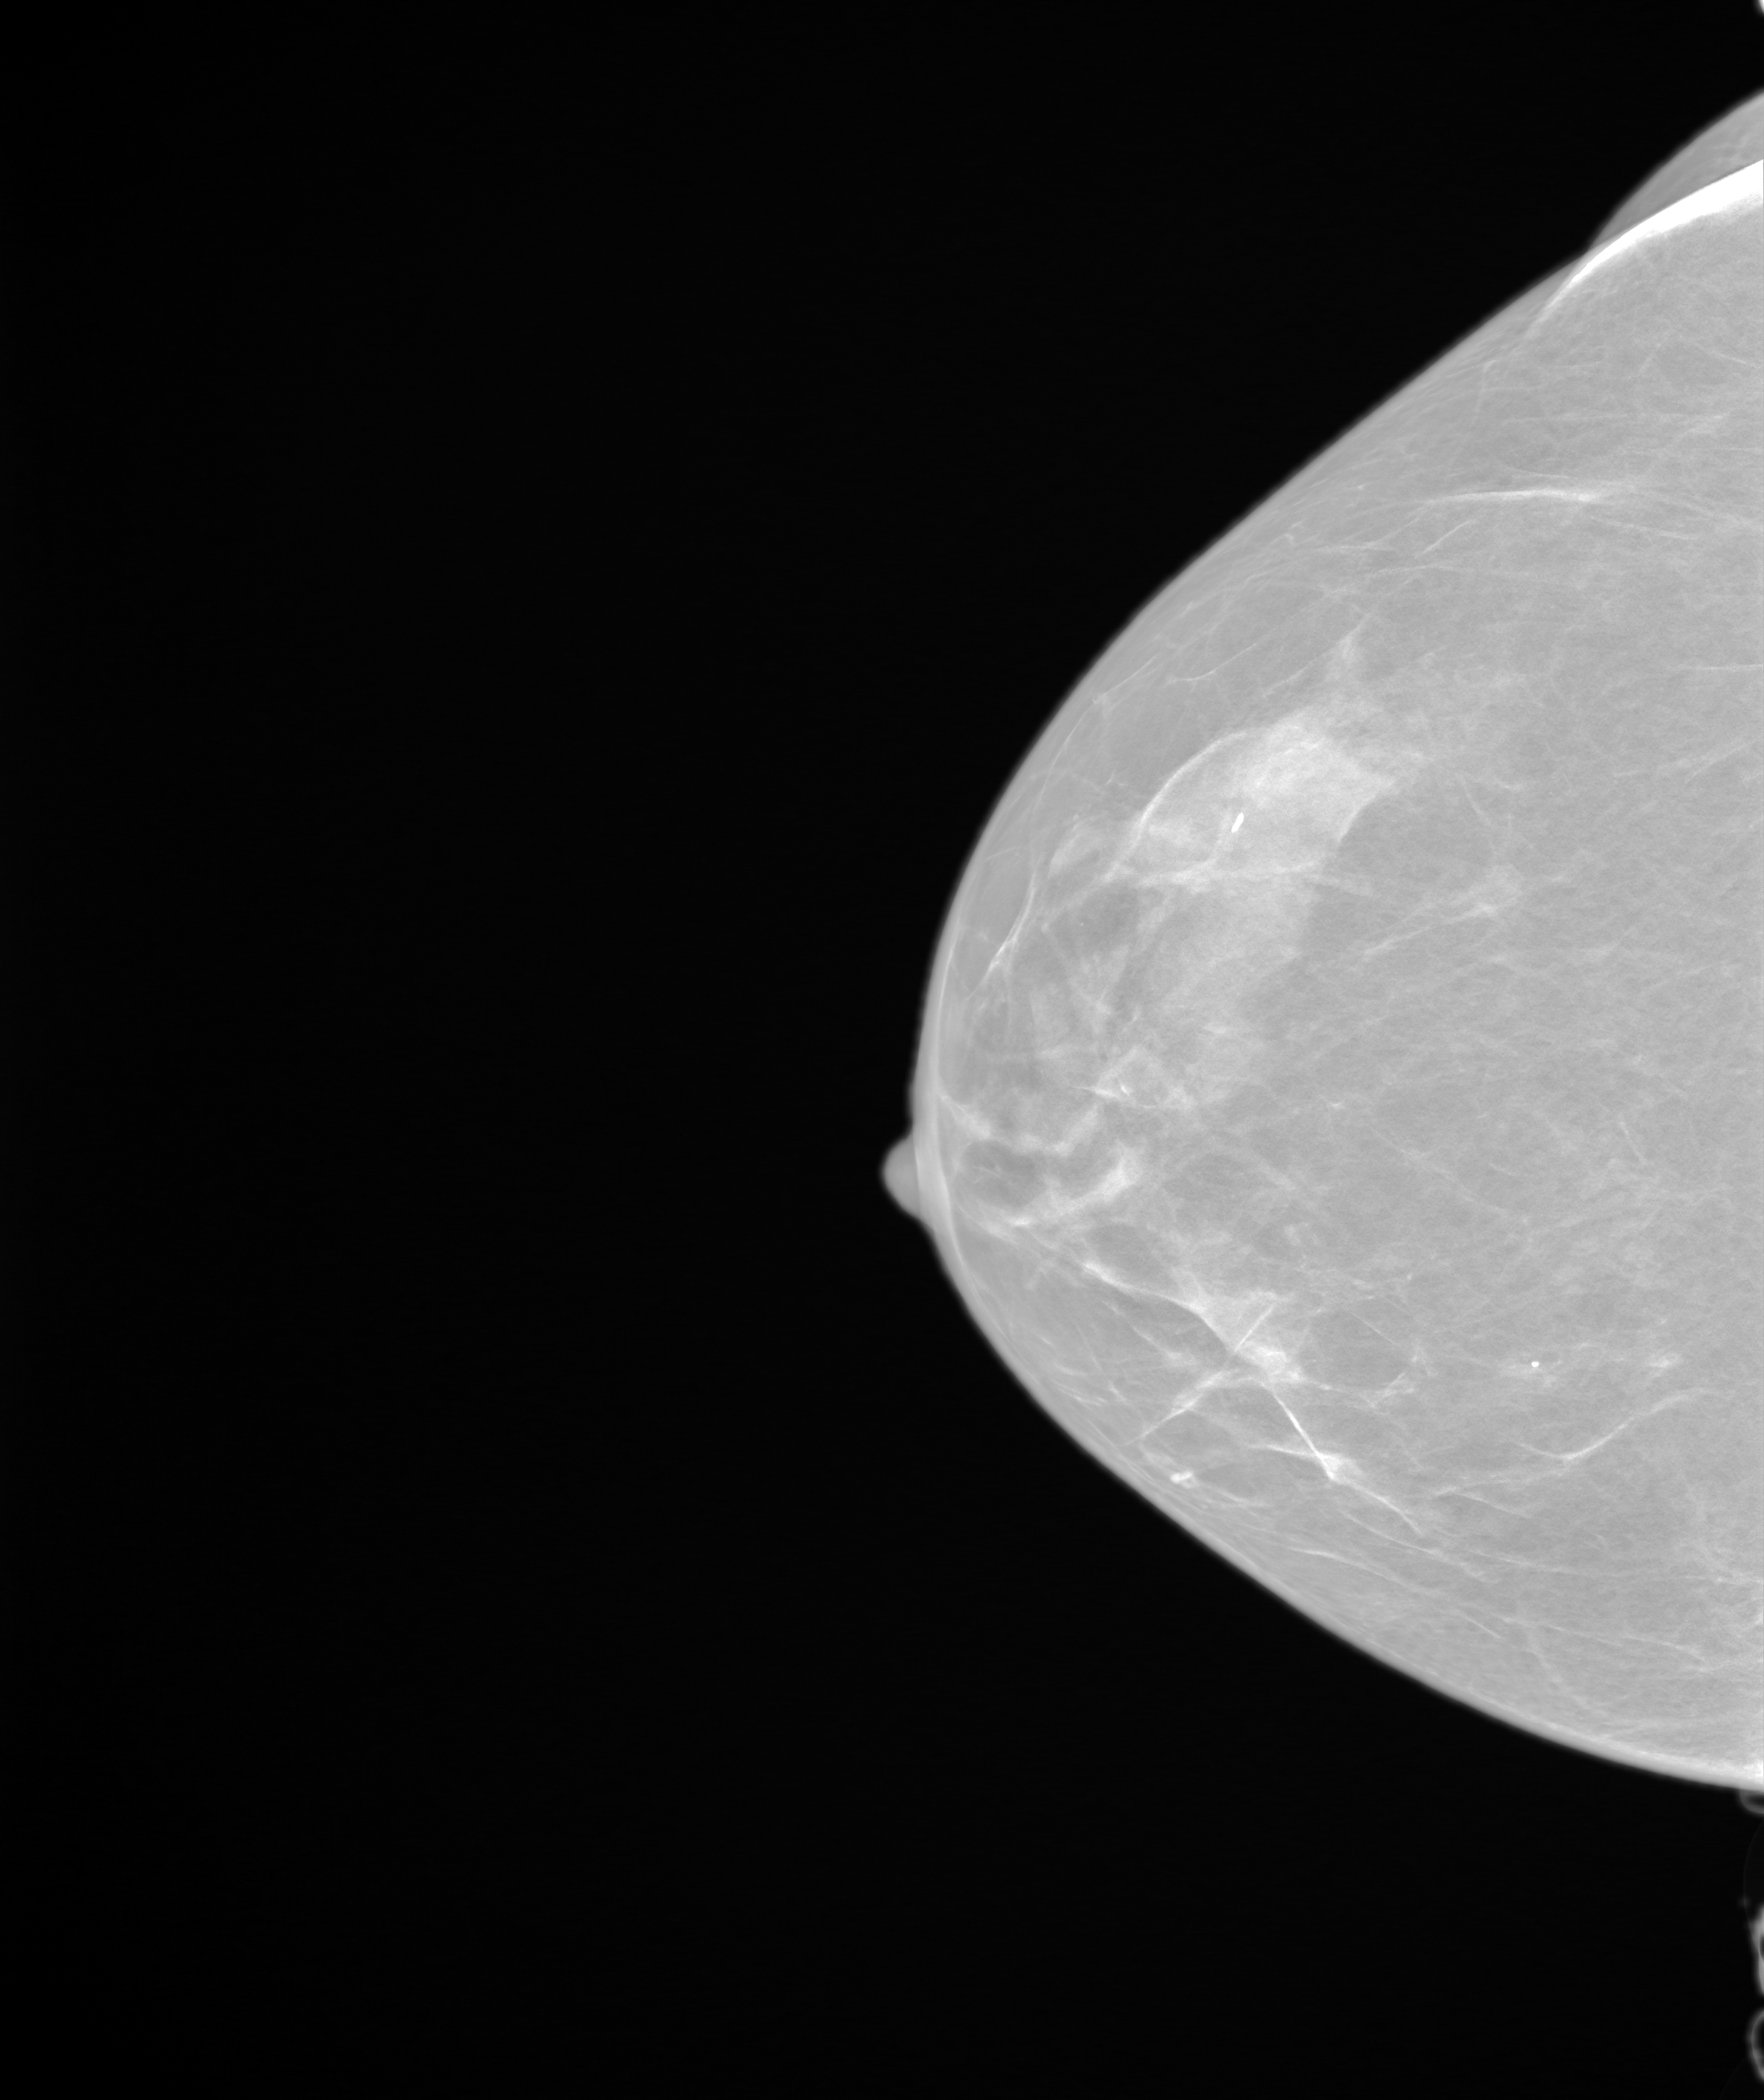
Screening examination; system: SenoIris_1SP2(440). Female patient, age 49 years.
Image type: synthesized 2-D view from tomosynthesis. Breast: right. Projection: cranio-caudal projection.